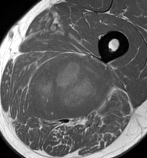
MRI of an extremity soft-tissue mass, one axial slice. Position 72 of 86 along the scan axis. MR volume resampled by the dataset authors to the PET/CT grid (not the native acquisition matrix). 3.27 mm slice thickness. 147 × 158 image matrix, field of view 144 × 154 mm. Male patient. Case-level facts recorded for this patient, not image findings: histological type: undifferentiated pleomorphic liposarcoma; grade: high; site of the primary tumour: left thigh.
Structures marked on this image (expert contour drawn on MRI and transferred to this co-registered scan by the dataset authors):
- gross tumour volume including surrounding oedema: box from (x=21, y=58) to (x=111, y=127) px
- gross tumour volume (mass): (x=30, y=60)–(x=109, y=120)